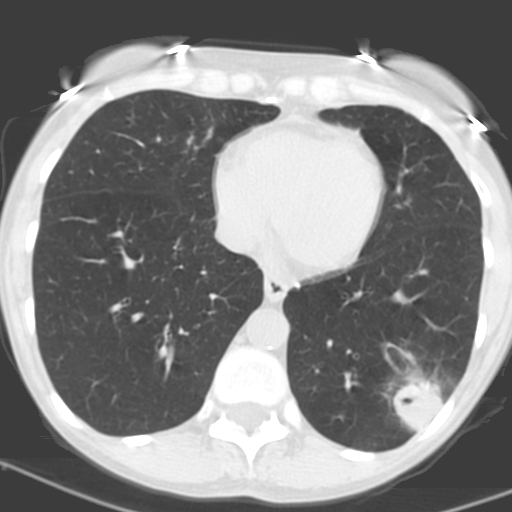
Chest CT (low-dose screening protocol), one axial image; baseline screening round; lung window (W 1500 / L -600 HU); 120 kVp; slice 102 of 156 in the series. Female participant, aged 56 years at enrolment. Current smoker at enrolment.
• Expert reader's lesion annotation, box from (x=377, y=363) to (x=457, y=434) px.
• The exam's reader record, not a measurement of the box and not confirmed to be the same lesion: non-calcified nodule or mass ≥4 mm, left lower lobe, 31 × 23 mm, poorly defined margins, soft tissue attenuation, pre-existing on the prior screen: no.
• Official screen result: positive, change unspecified: nodule(s) >= 4 mm or enlarging nodule(s), mass(es), or other non-specific abnormalities suspicious for lung cancer.
• Participant outcome: lung cancer diagnosed 27 days after this screen — squamous cell carcinoma, NOS, left lower lobe, poorly differentiated (G3), stage IB (AJCC 6th edition), 35 mm at pathology.